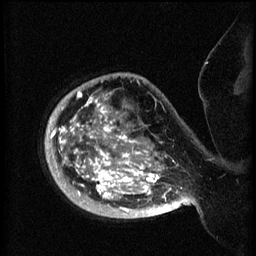
Breast MRI (dynamic contrast-enhanced), one sagittal slice; 3 images stored at this slice position (order not interpretable as contrast timing); 1.5 T; TE 4.2 ms, TR 8.2 ms; 2 mm slice thickness; 256 × 256 image matrix, field of view 200 × 200 mm. Female patient, age 50 years.
Structures marked on this image (semi-automatically segmented with operator editing):
- analysis volume of interest (the breast-tissue region the enhancement analysis was run in; not a lesion): bounding box <46,74,173,219> (left, top, right, bottom; pixels)
- tumour enhancement mask (voxels above the 70 % enhancement threshold inside the analysis volume of interest): <47,92,173,213>